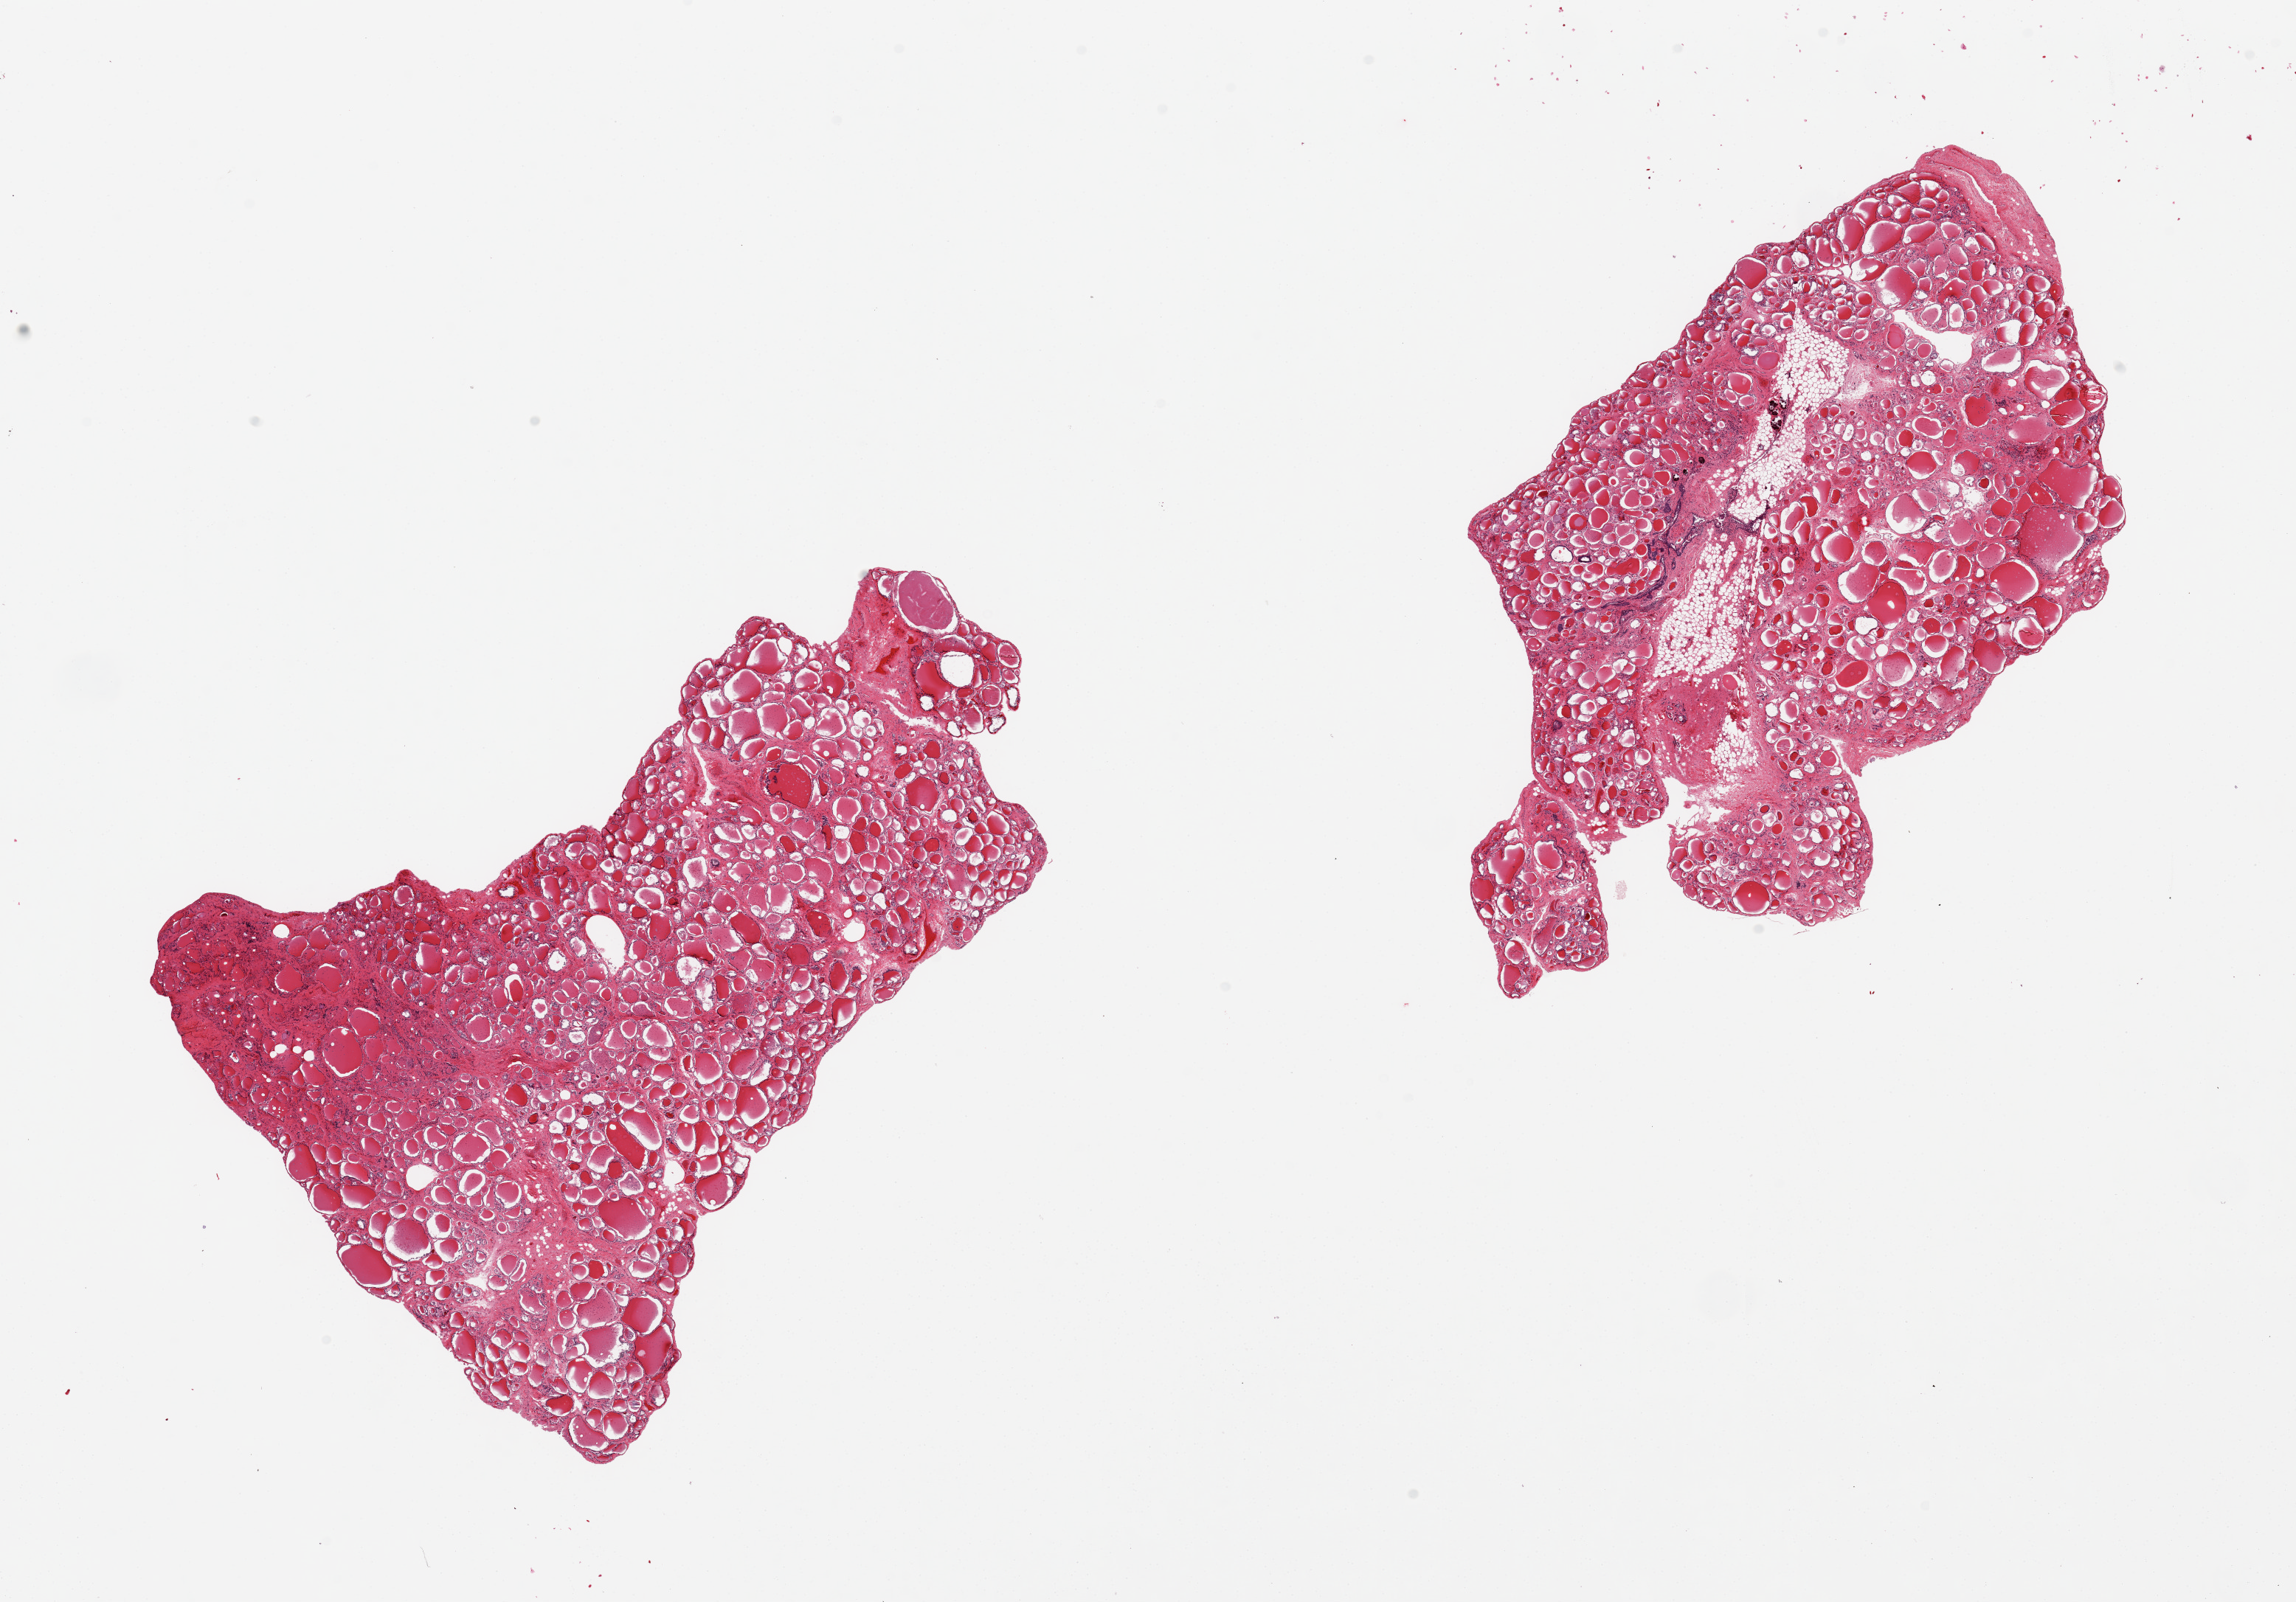
Digitized haematoxylin and eosin-stained section, a low-resolution overview of the entire scanned area, about 24.6 x 17.2 mm (slide scanned at 20x). Donor sex: male.
Specimen: PAXgene-fixed paraffin-embedded (PFPE) section; sampled site (target tissue): thyroid; tissue donor sample.